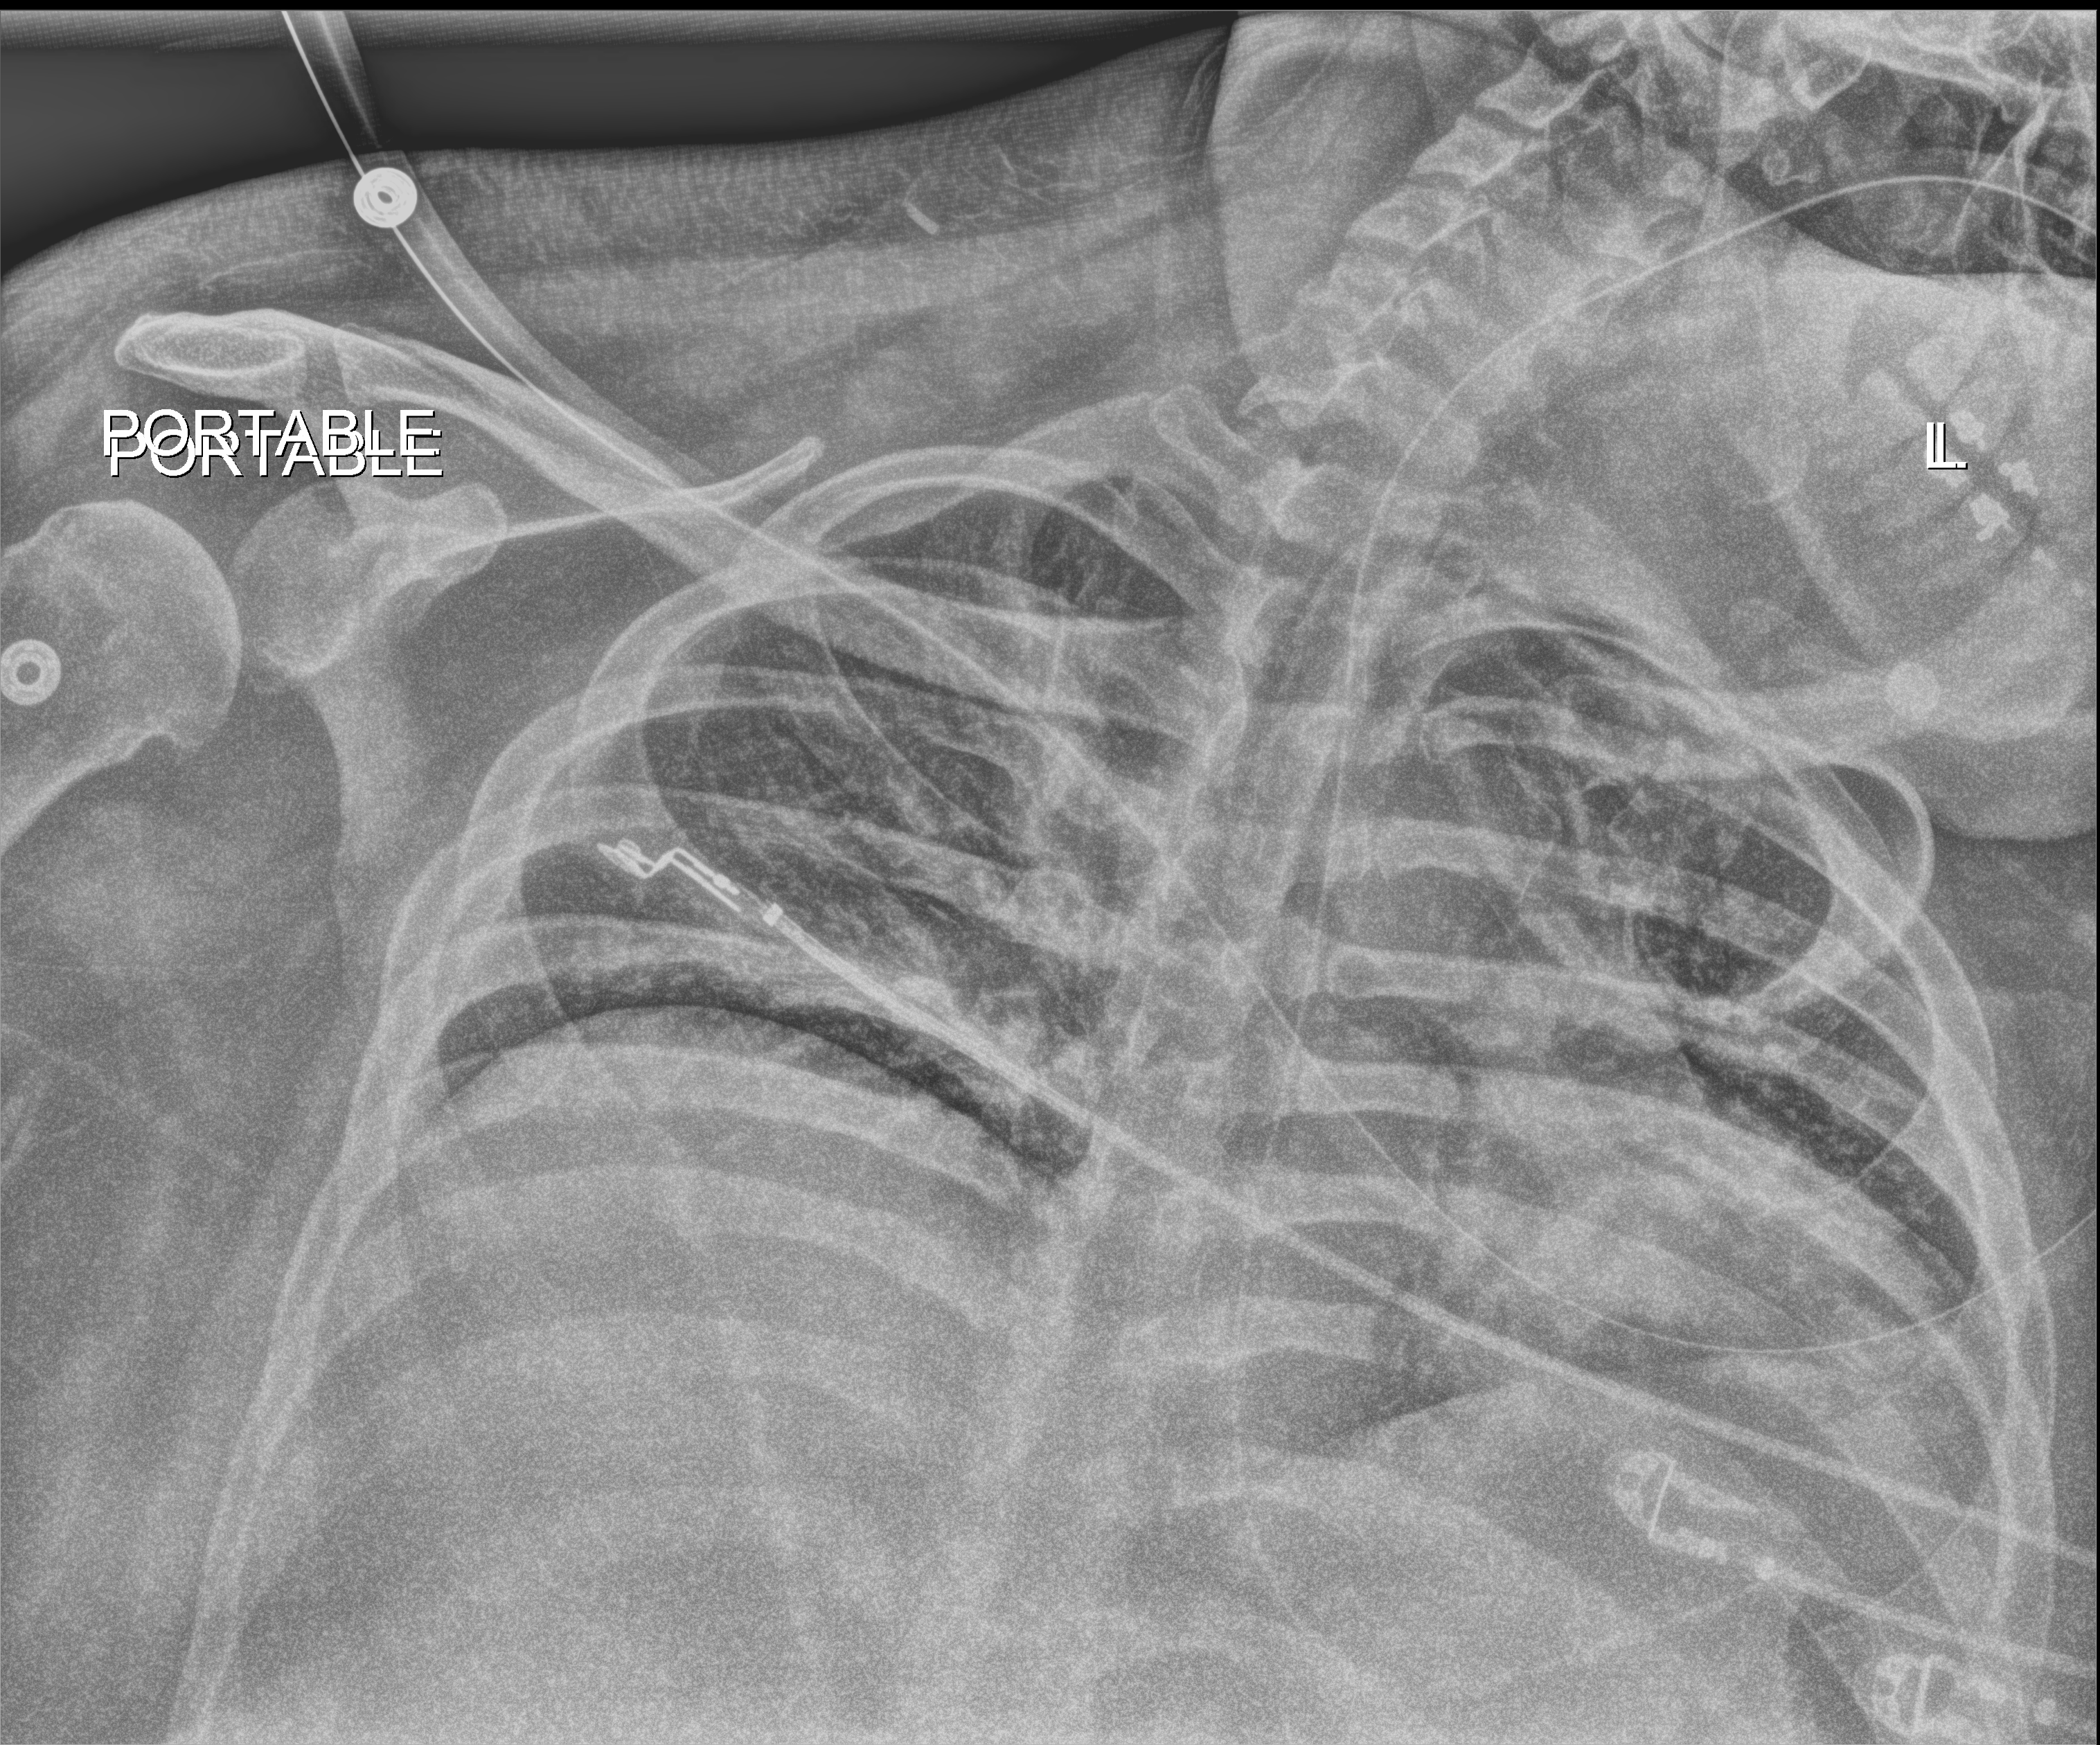
Chest X-ray (portable); anteroposterior (AP) projection. Male patient hospitalised with COVID-19, age 18–59 years.
Hospital-stay facts (about this admission, not read from this image; timing relative to this image not recorded): mechanically ventilated during this hospital stay: yes; length of hospital stay: 69 days.